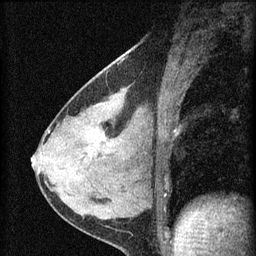
Breast MRI (dynamic contrast-enhanced), one sagittal slice; position 29 of 60 along the scan axis; dynamic contrast-enhanced series, image 2 of 4 at this slice position (ordered by acquisition); 1.5 T; TE 4.2 ms, TR 8.2 ms; 256 × 256 image matrix, field of view 180 × 180 mm. Female patient, age 37 years.
Outlined on this slice (semi-automatically segmented with operator editing):
- analysis volume of interest (the breast-tissue region the enhancement analysis was run in; not a lesion): bounding box [x1, y1, x2, y2] px = [77, 116, 127, 175]
- tumour enhancement mask (voxels above the 70 % enhancement threshold inside the analysis volume of interest): [95, 141, 99, 145]